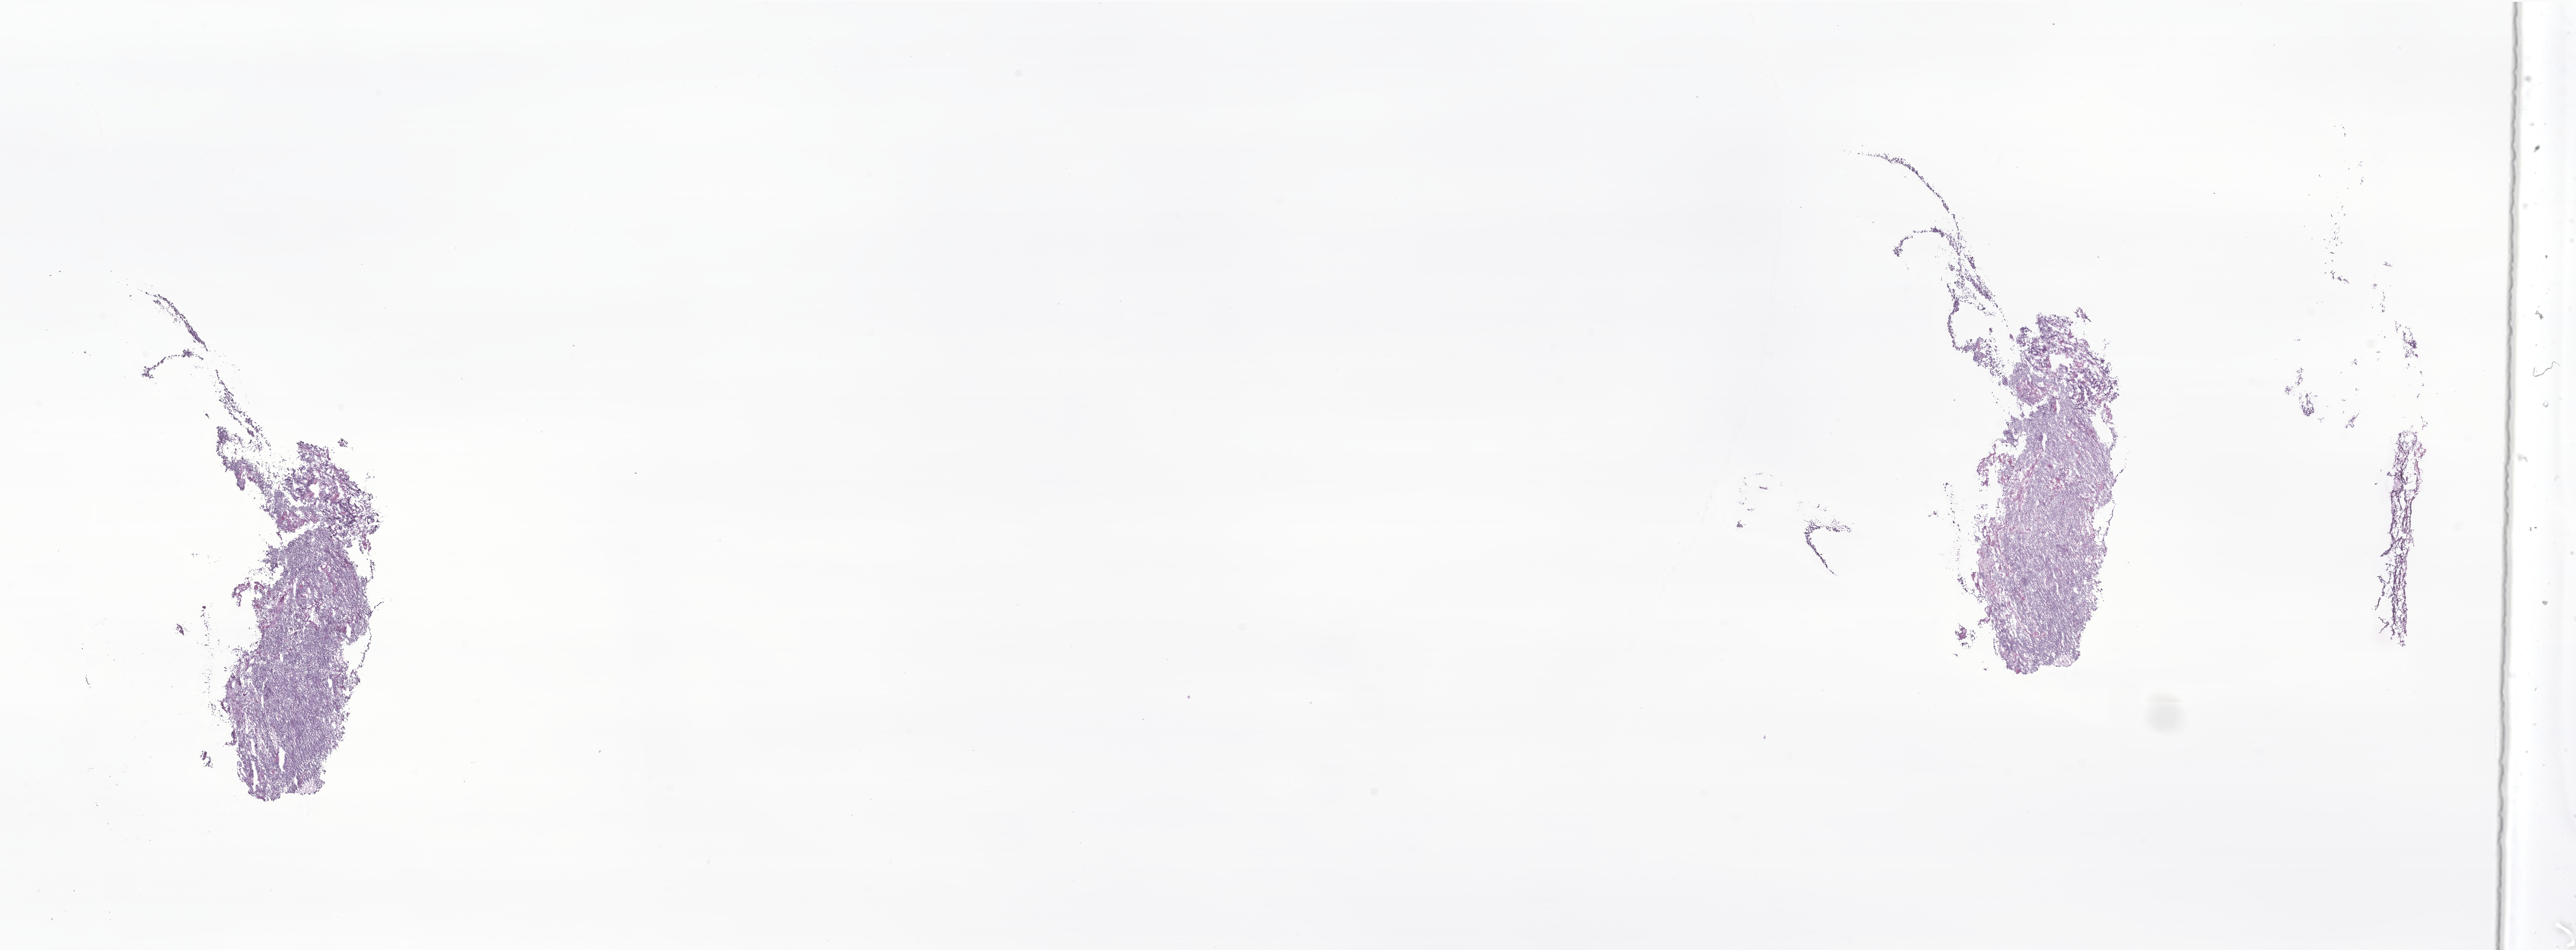
Digitized hematoxylin and eosin (H&E)-stained section of tumor tissue from the brain — whole scanned area (about 33.0 x 12.2 mm) shown as a low-resolution overview, frozen section. Male patient, age 803 days (about 2.2 years).
Diagnosis (ICD-O-3 morphology term): Medulloblastoma, NOS.